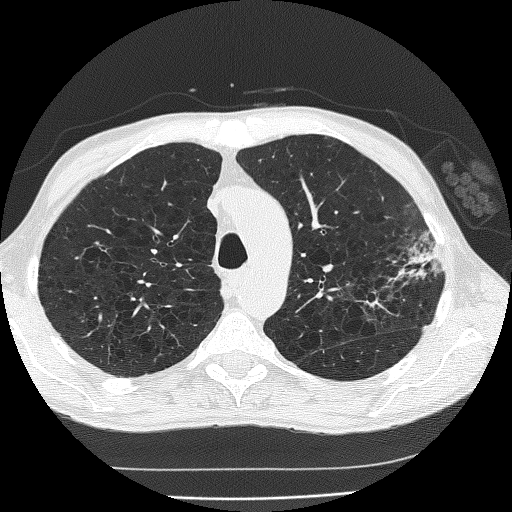
Chest CT (low-dose screening protocol), one axial image. Second annual screen. Lung window (W 1500 / L -600 HU). Lung (sharp) reconstruction kernel (FC51). Male, age 60 years at enrolment.
Expert-annotated lung lesion, bounding box [x1, y1, x2, y2] px = [346, 231, 448, 334]. The screening reader recorded 2 non-calcified nodules or masses ≥4 mm on this exam (left upper lobe, left upper lobe); which of them this box marks is not recorded. Later outcome: lung cancer diagnosed 178 days after this screen — bronchiolo-alveolar carcinoma, mucinous, left upper lobe, stage IV (AJCC 6th edition).